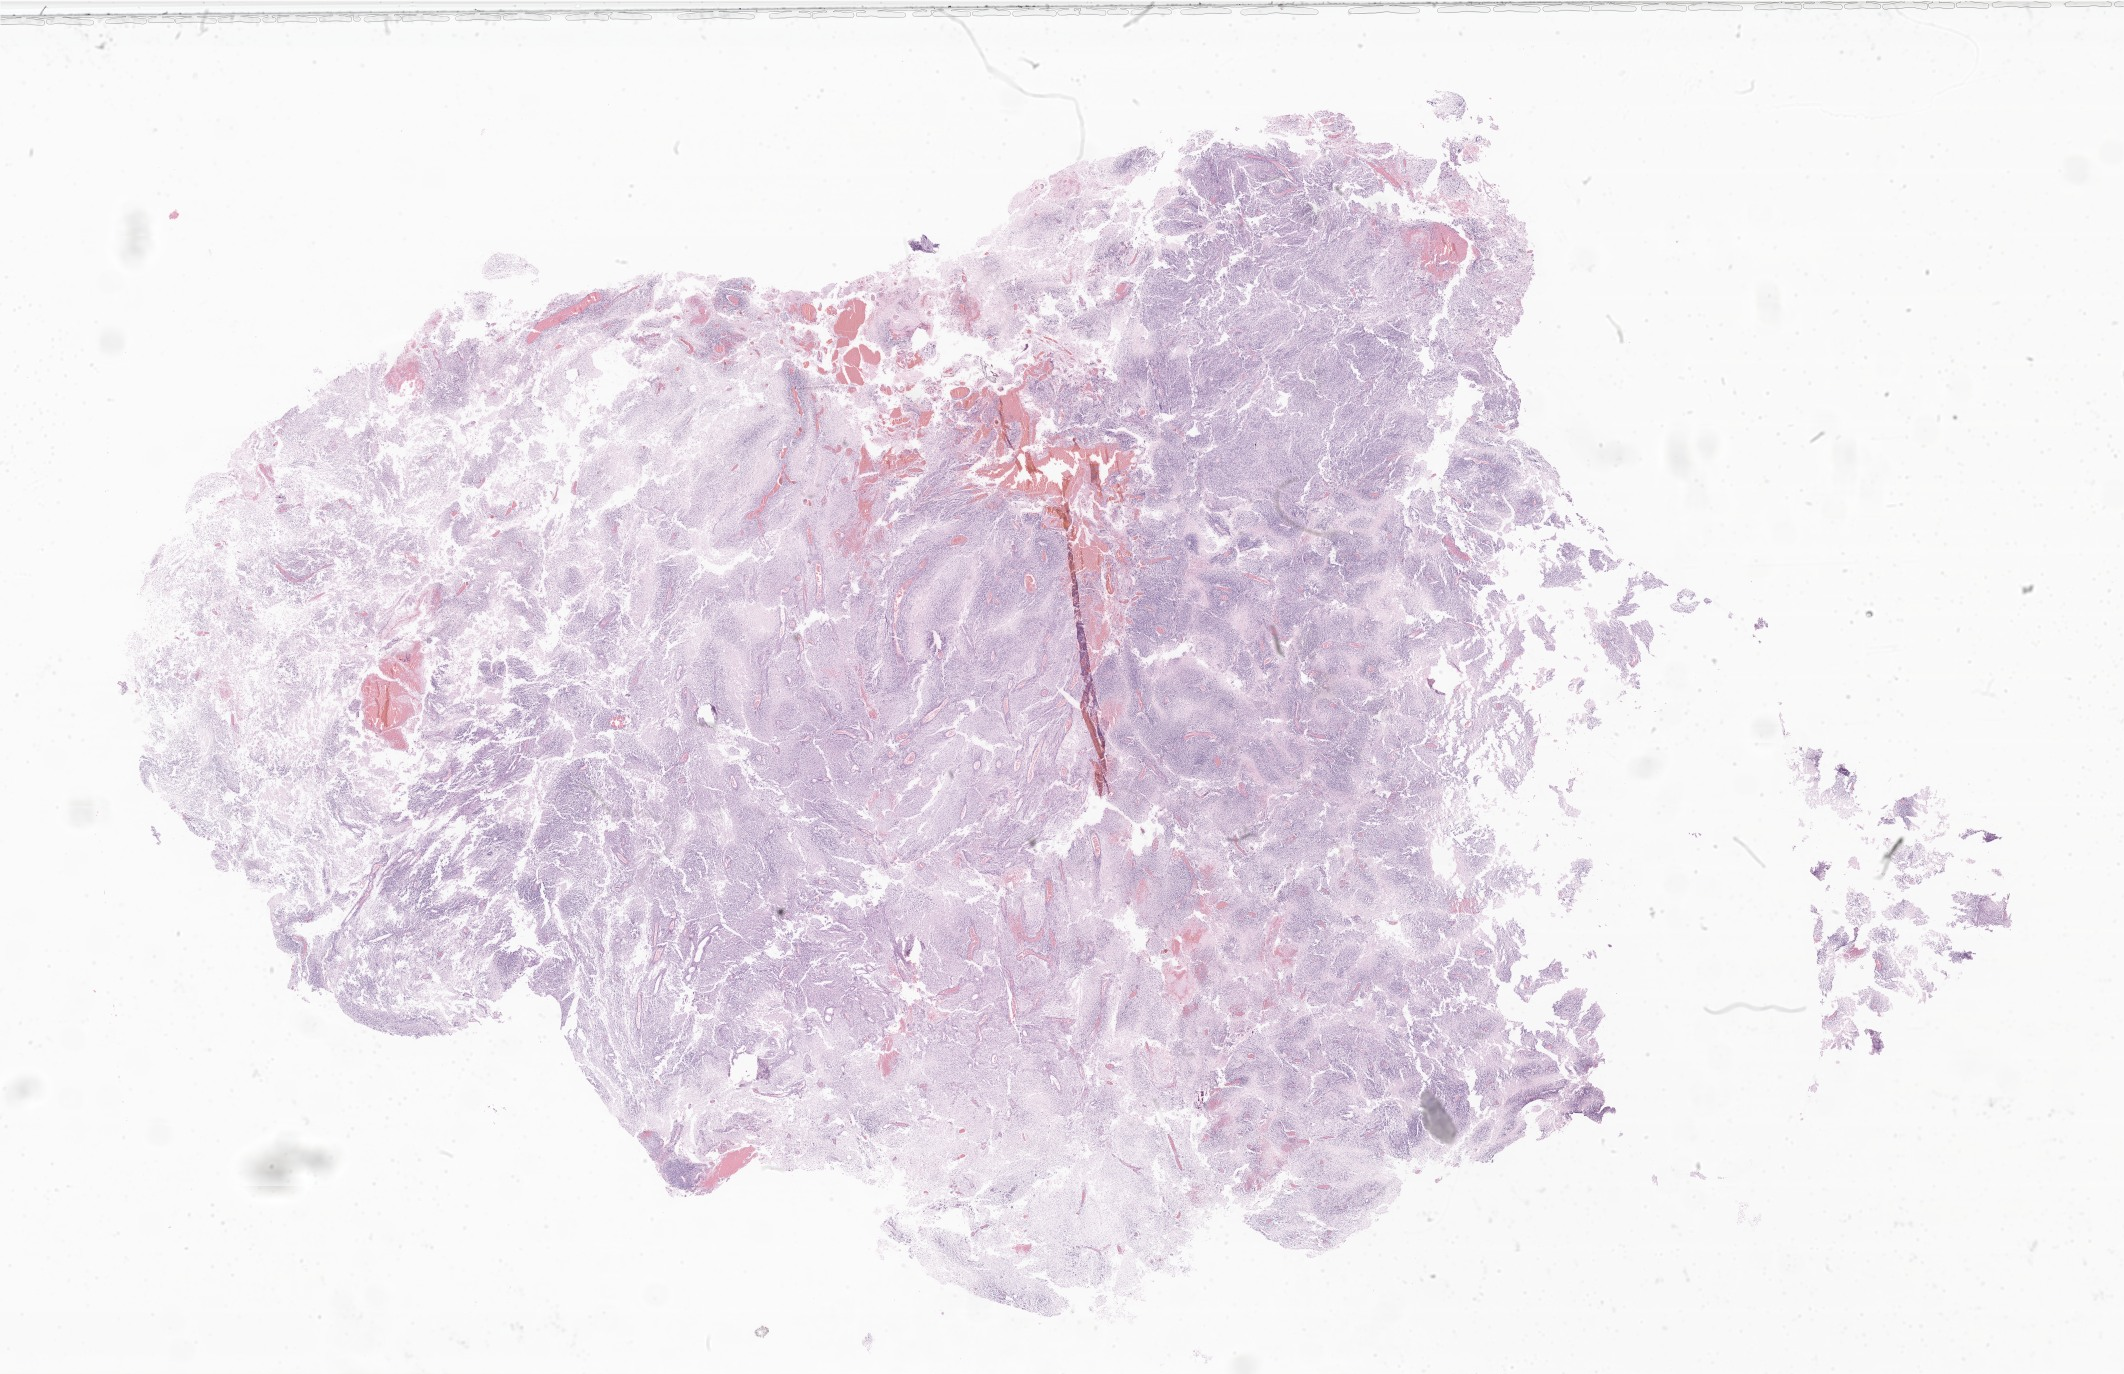
Whole-slide image, H&E stain of tumor tissue from the brain, low-resolution overview of the scanned area, about 35.8 x 23.2 mm. FFPE section. Patient: female, age 38 months.
Recorded diagnosis: Neoplasm, malignant.